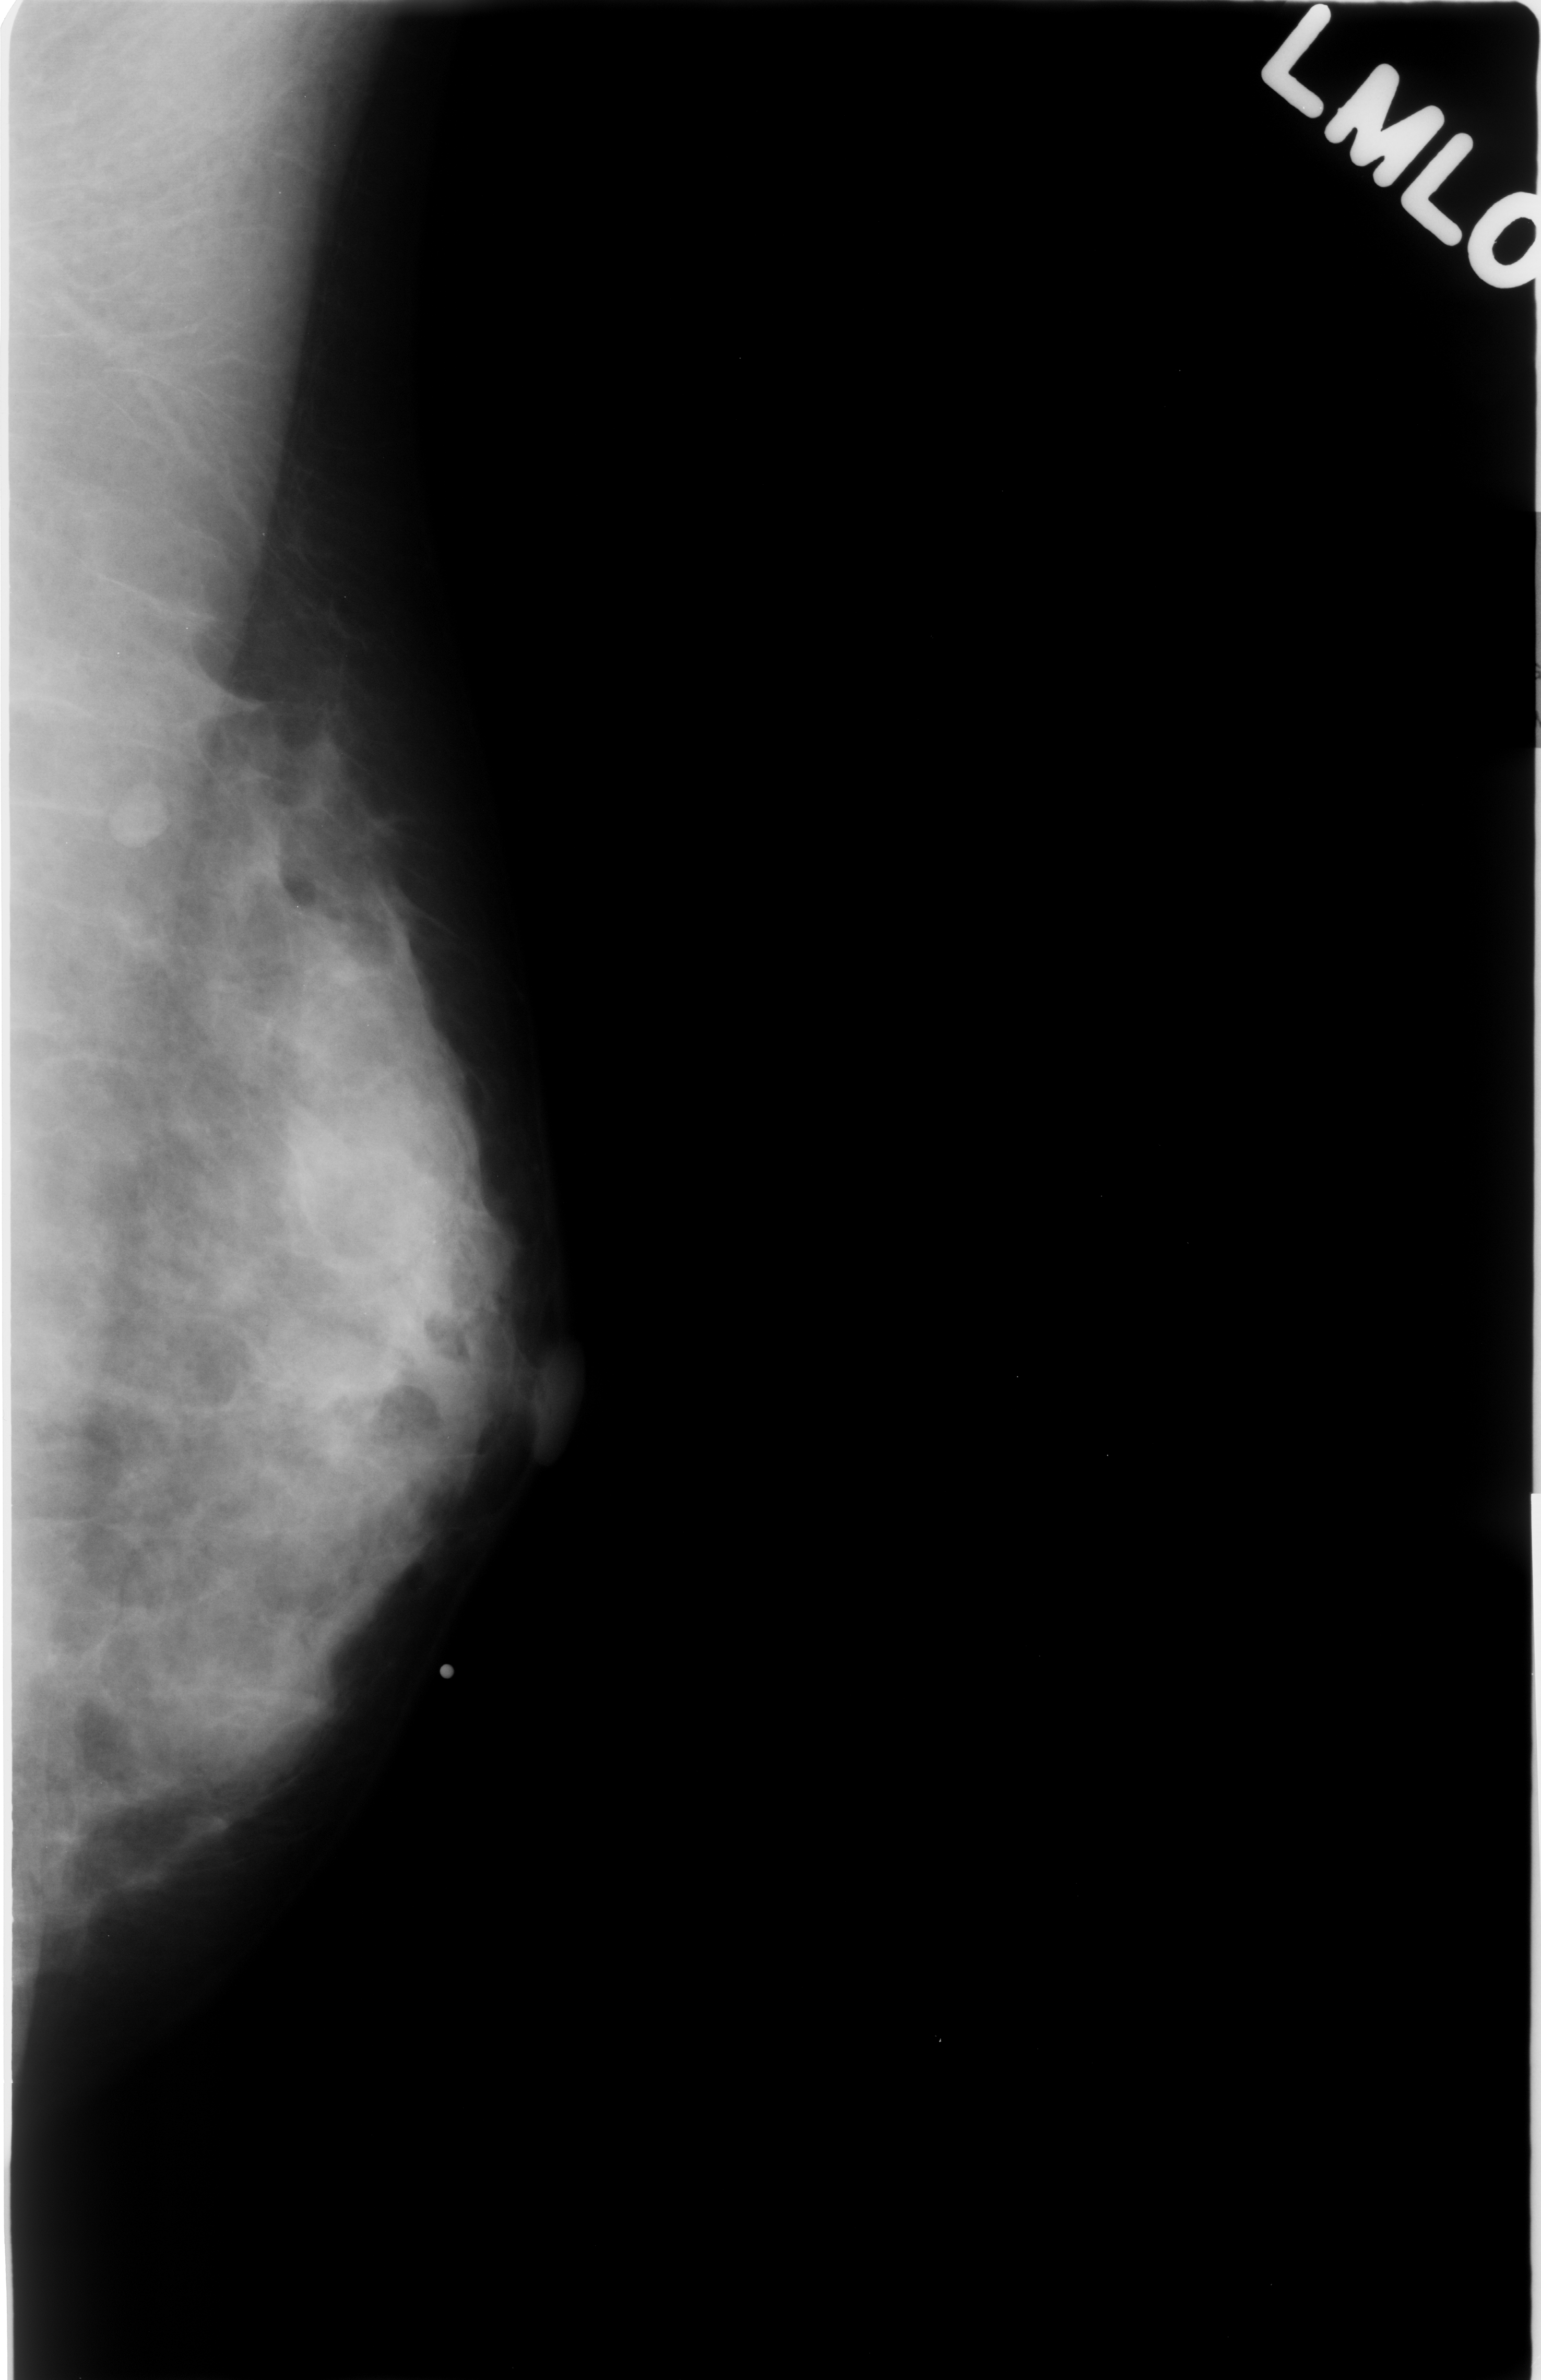
Digitized screen-film mammogram; left breast; MLO view; BI-RADS breast density category 3 (scale 1–4); 1541 × 2380 image matrix.
Expert-marked regions of interest on this image (one box per marked abnormality):
- mass, shape round, margins obscured; BI-RADS assessment category 4; subtlety rating 2 on a 1 (subtle) to 5 (obvious) scale; pathology result (as recorded, not read from the image): benign: box from (x=218, y=1590) to (x=359, y=1753) px